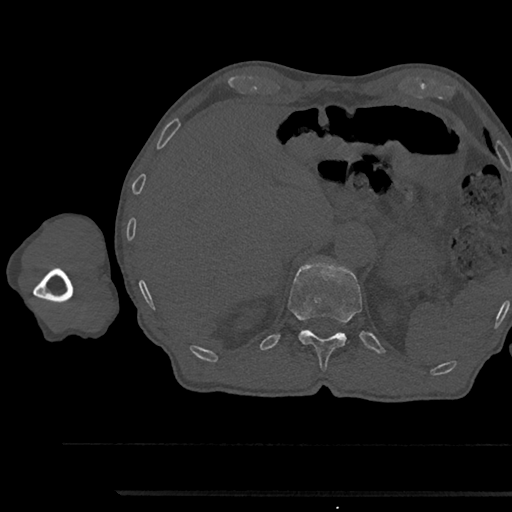
CT including the spine, one axial slice; position 706 of 797 along the scan axis; bone window (W 1800 / L 400 HU); 512 × 512 image matrix. Male patient, age 79 years. From the clinical record (not read from this slice): primary cancer: prostate.
Annotated regions visible in this slice (semi-automatically segmented with operator editing):
- T12 vertebra: bounding box <288,263,362,370> (left, top, right, bottom; pixels)